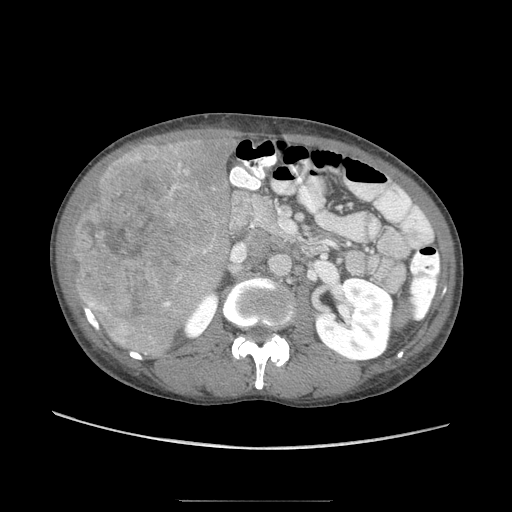
Contrast-enhanced abdominal CT (liver protocol), one axial slice; position 29 of 103 along the scan axis; soft-tissue window (W 400 / L 40 HU); 512 × 512 image matrix, field of view 380 × 380 mm. From the clinical record (not read from this slice): diagnosis: hepatocellular carcinoma (patient treated with transarterial chemoembolisation; whether this scan precedes or follows treatment is not stated here); TNM stage (as recorded): Stage-IIIA; Child-Pugh class: A; tumour differentiation: moderately differentiated; tumour nodularity: multinodular.
Outlined on this slice (semi-automatically segmented with operator editing):
- liver parenchyma outside the tumour (the mass and vessels are separate outlines, so this box may not span the whole liver): bounding box <92,136,236,353> (left, top, right, bottom; pixels)
- mass: <66,141,220,343>